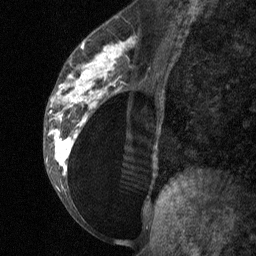
Breast MRI (dynamic contrast-enhanced), one sagittal slice; position 34 of 64 along the scan axis; dynamic contrast-enhanced study with each time point stored as its own series, time point 2 of 3 at this slice position (early post-contrast, ordered by acquisition time); 1.5 T; TE 4.8 ms, TR 27 ms; 2 mm slice thickness; 256 × 256 image matrix, field of view 180 × 180 mm. Female patient, age 34 years. From the clinical record (not read from this slice): setting: breast cancer imaged before/during neoadjuvant chemotherapy; receptor status: HR-positive, HER2-negative.
Annotated regions visible in this slice (semi-automatically segmented with operator editing):
- analysis volume of interest (the breast-tissue region the enhancement analysis was run in; not a lesion): box from (x=43, y=23) to (x=157, y=197) px
- tumour enhancement mask (voxels above the 90 % enhancement threshold inside the analysis volume of interest): (x=49, y=39)–(x=133, y=175)